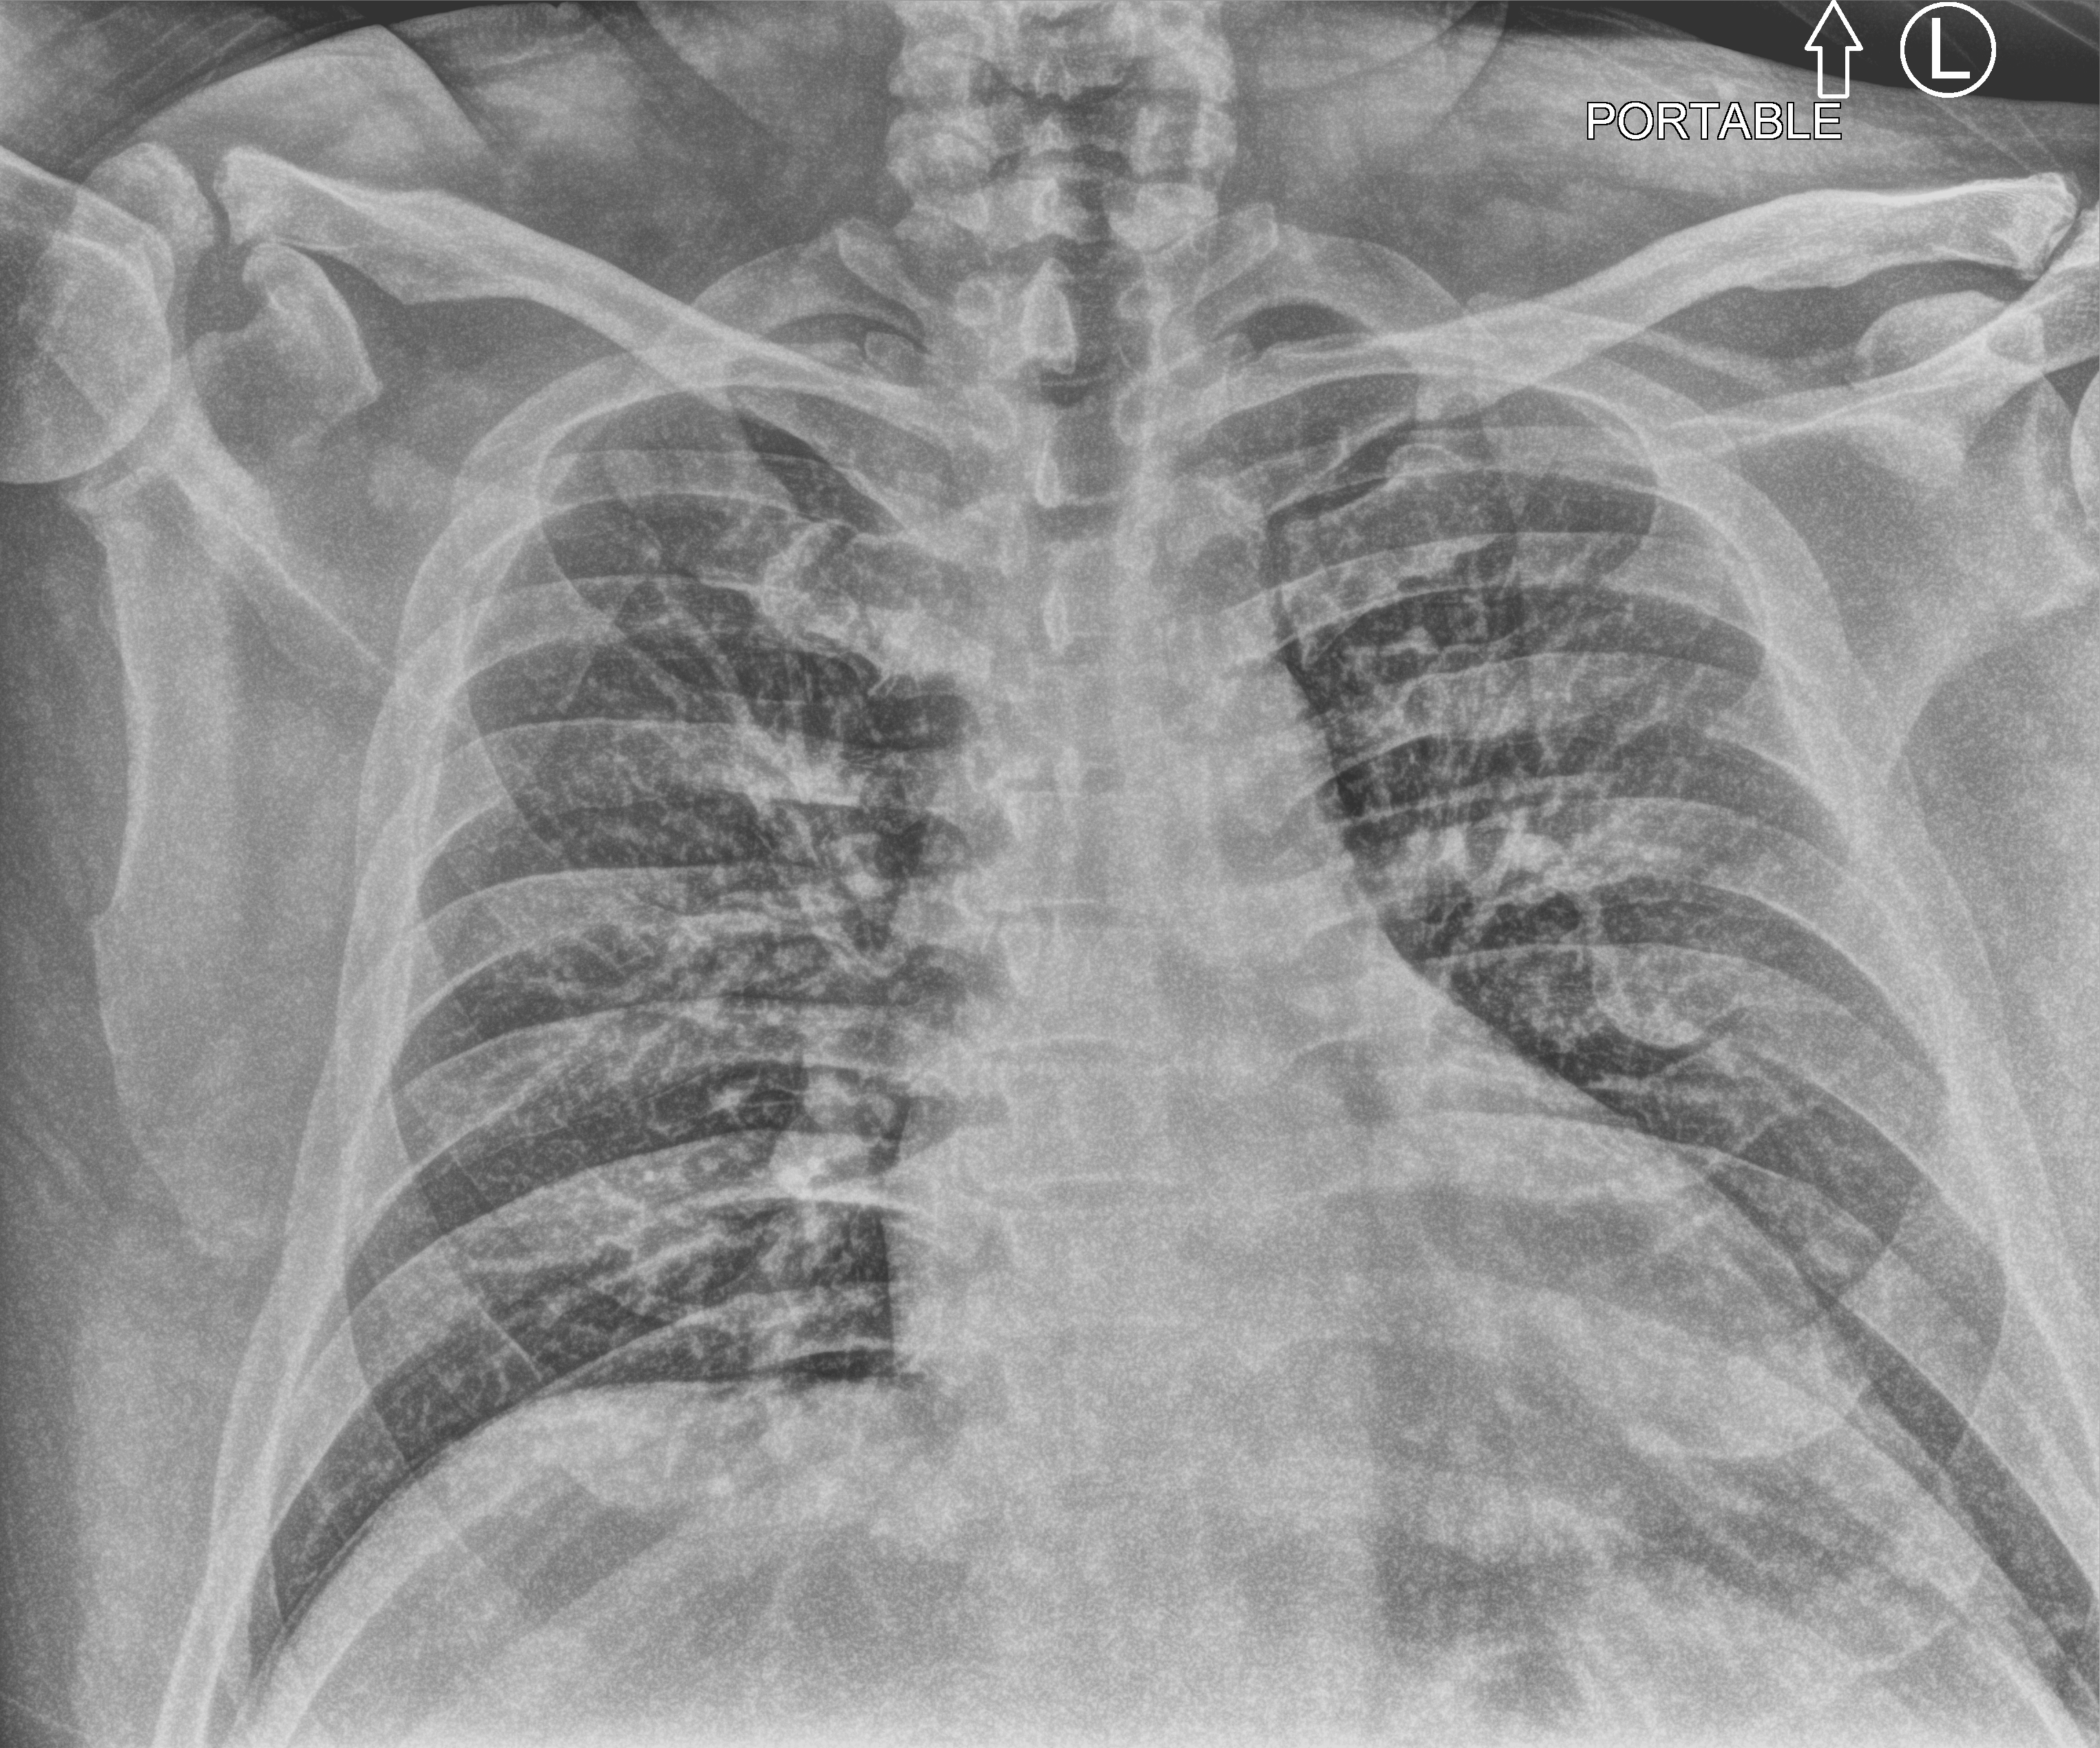
Portable chest radiograph, anteroposterior (AP) projection. Patient hospitalised with COVID-19; male, aged 18–59 years.
From the hospital-stay record, not from the radiograph (when in the stay this image was taken is not recorded):
- mechanically ventilated during this hospital stay: no
- admitted to intensive care during this hospital stay: no